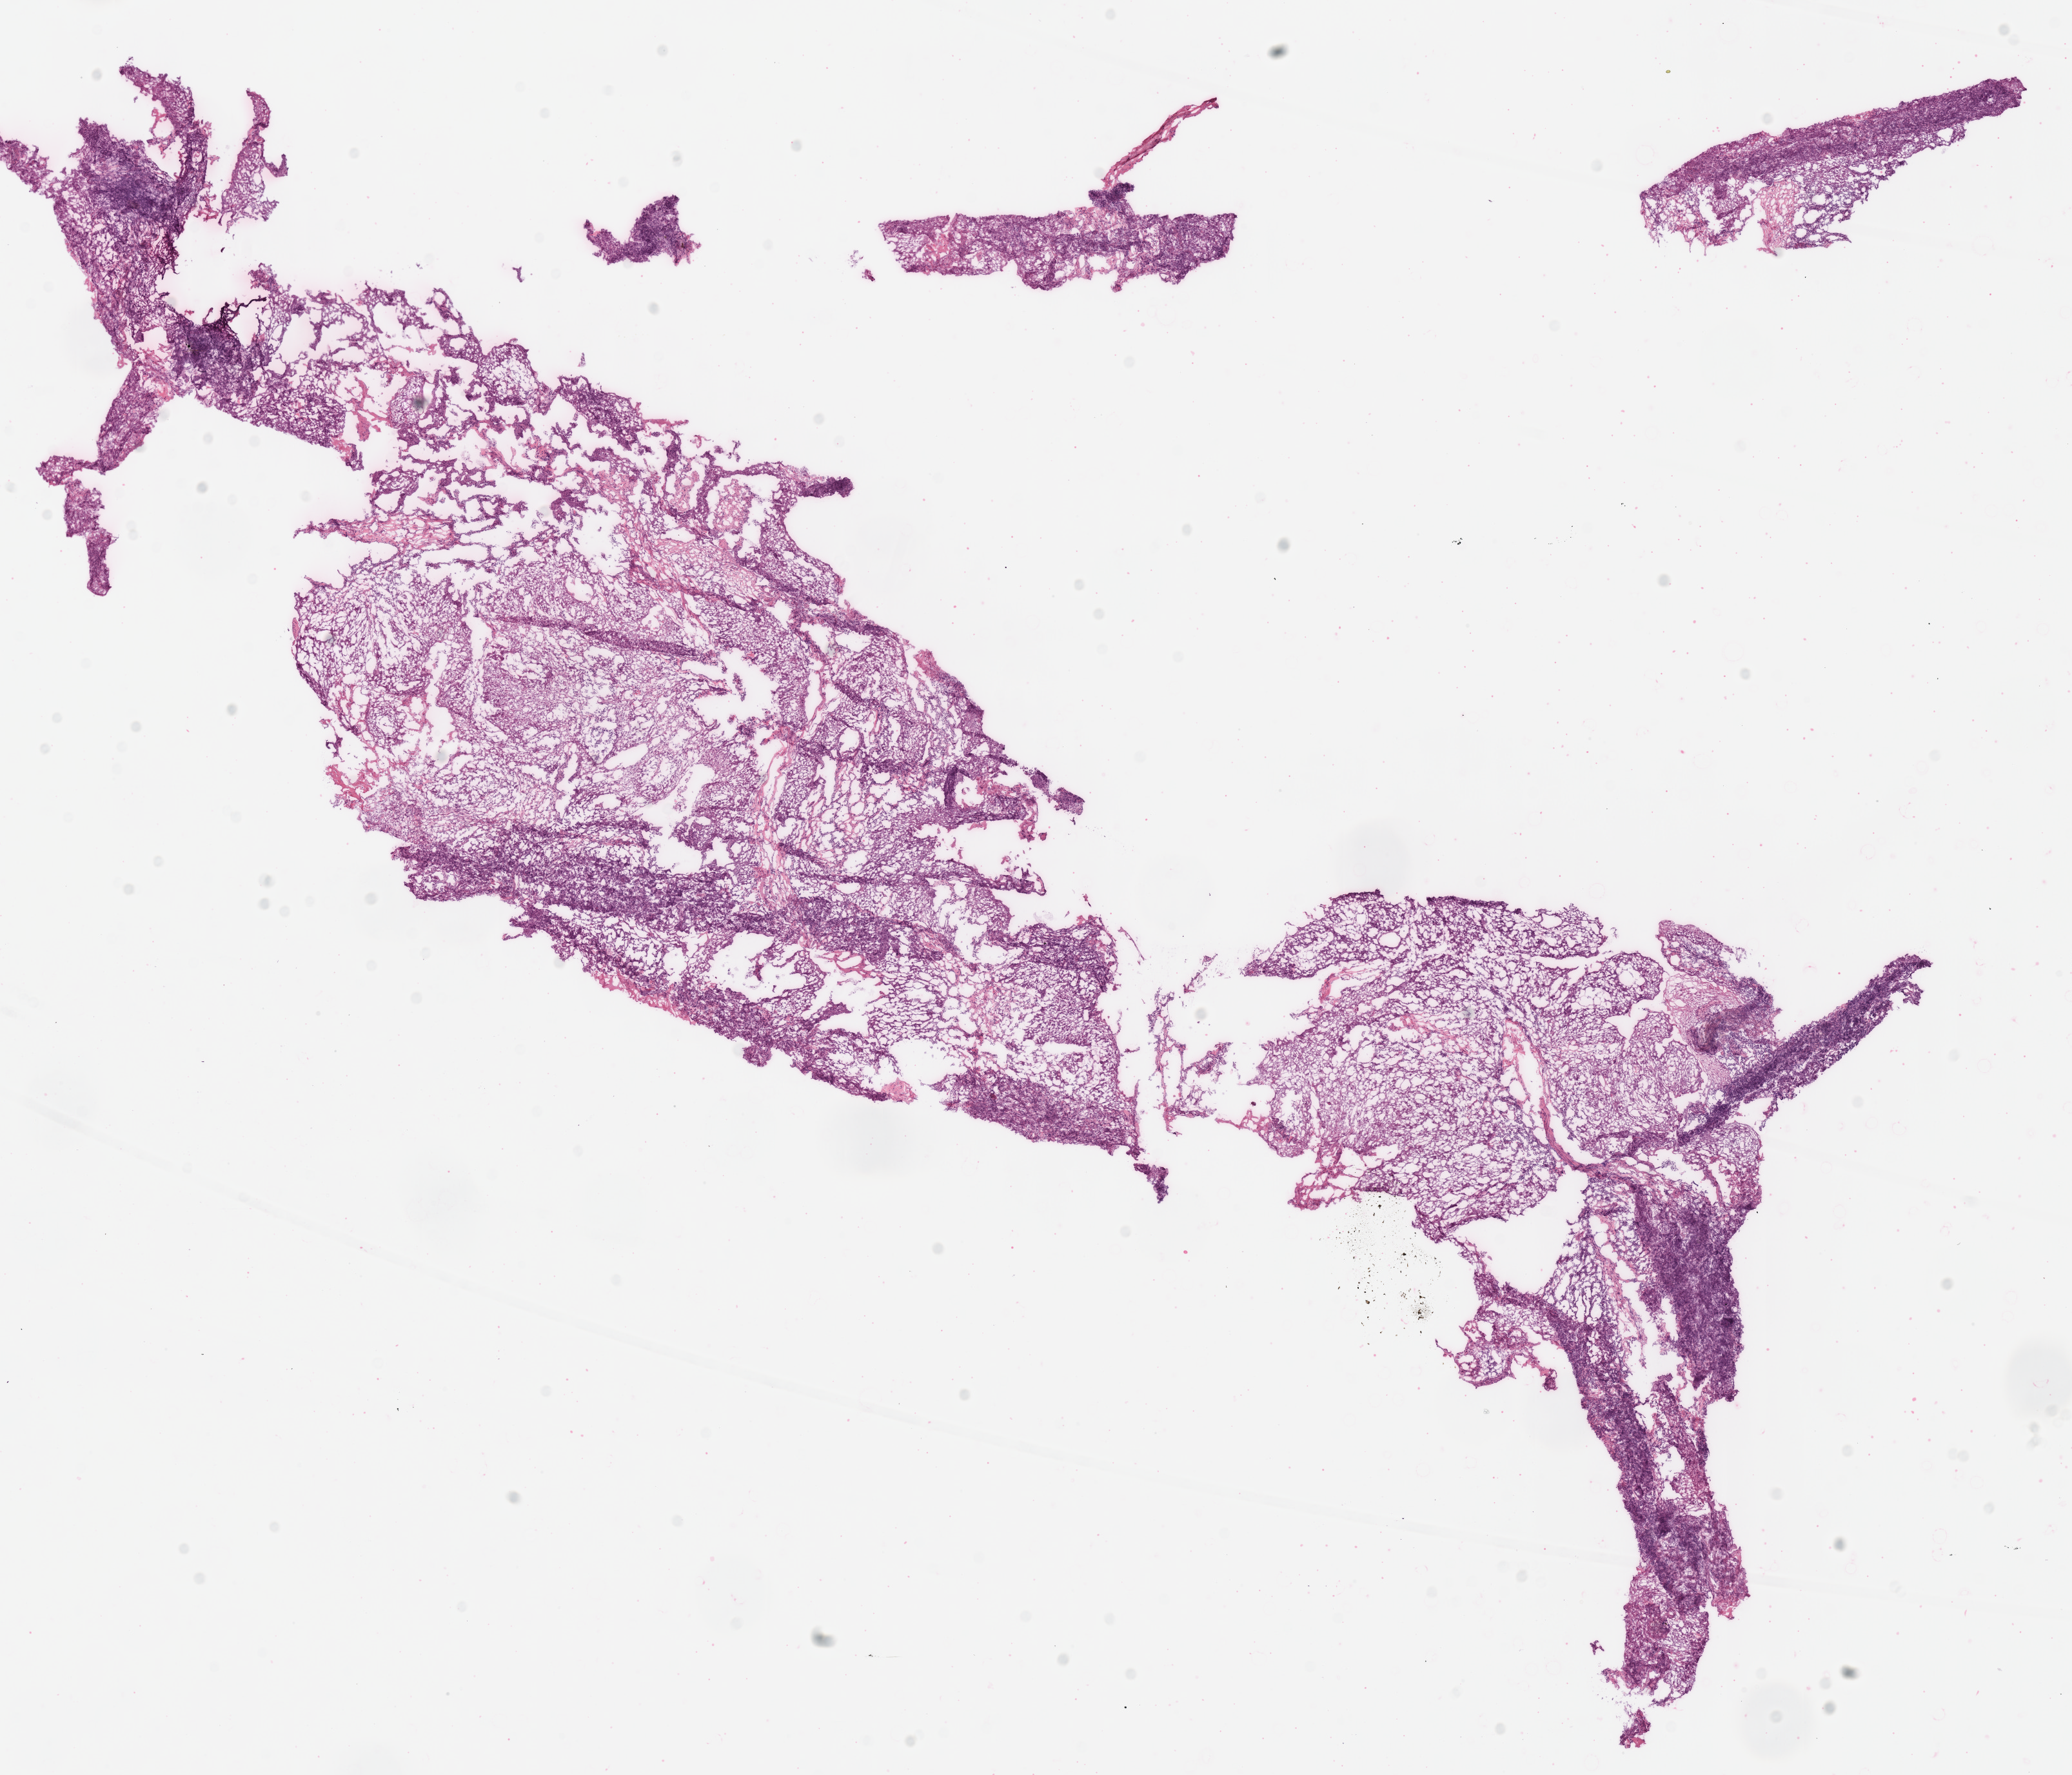
Digitized Hematoxylin and eosin (H&E) stained tissue section (whole slide) — low-resolution overview of the scanned area, about 12.7 x 10.8 mm (acquisition: 40x scan); frozen section from the top of the tissue portion; head and neck, primary tumour sample. Patient: male, age at initial diagnosis 65 years. Histologic grade: G3 (poorly differentiated). Pathologist review of this section (percent, as recorded): tumour cells 100%, tumour nuclei 72%, normal cells 0%, stromal cells 0%, necrosis 0%. Infiltration values recorded for this section: lymphocyte infiltration 15%, monocyte infiltration 2%, neutrophil infiltration 2%.
Diagnosis: Squamous cell carcinoma, NOS (overlapping lesion of lip, oral cavity and pharynx).